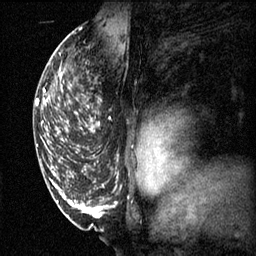
Breast MRI (dynamic contrast-enhanced), one sagittal slice. Position 38 of 60 along the scan axis. 3 images stored at this slice position (order not interpretable as contrast timing). 1.5 T. TE 4.2 ms, TR 11.1 ms. 256 × 256 image matrix, field of view 180 × 180 mm. Female patient, age 50 years.
Outlined on this slice (semi-automatically segmented with operator editing):
- analysis volume of interest (the breast-tissue region the enhancement analysis was run in; not a lesion): bounding box <68,68,101,141> (left, top, right, bottom; pixels)
- tumour enhancement mask (voxels above the 70 % enhancement threshold inside the analysis volume of interest): <68,96,100,133>